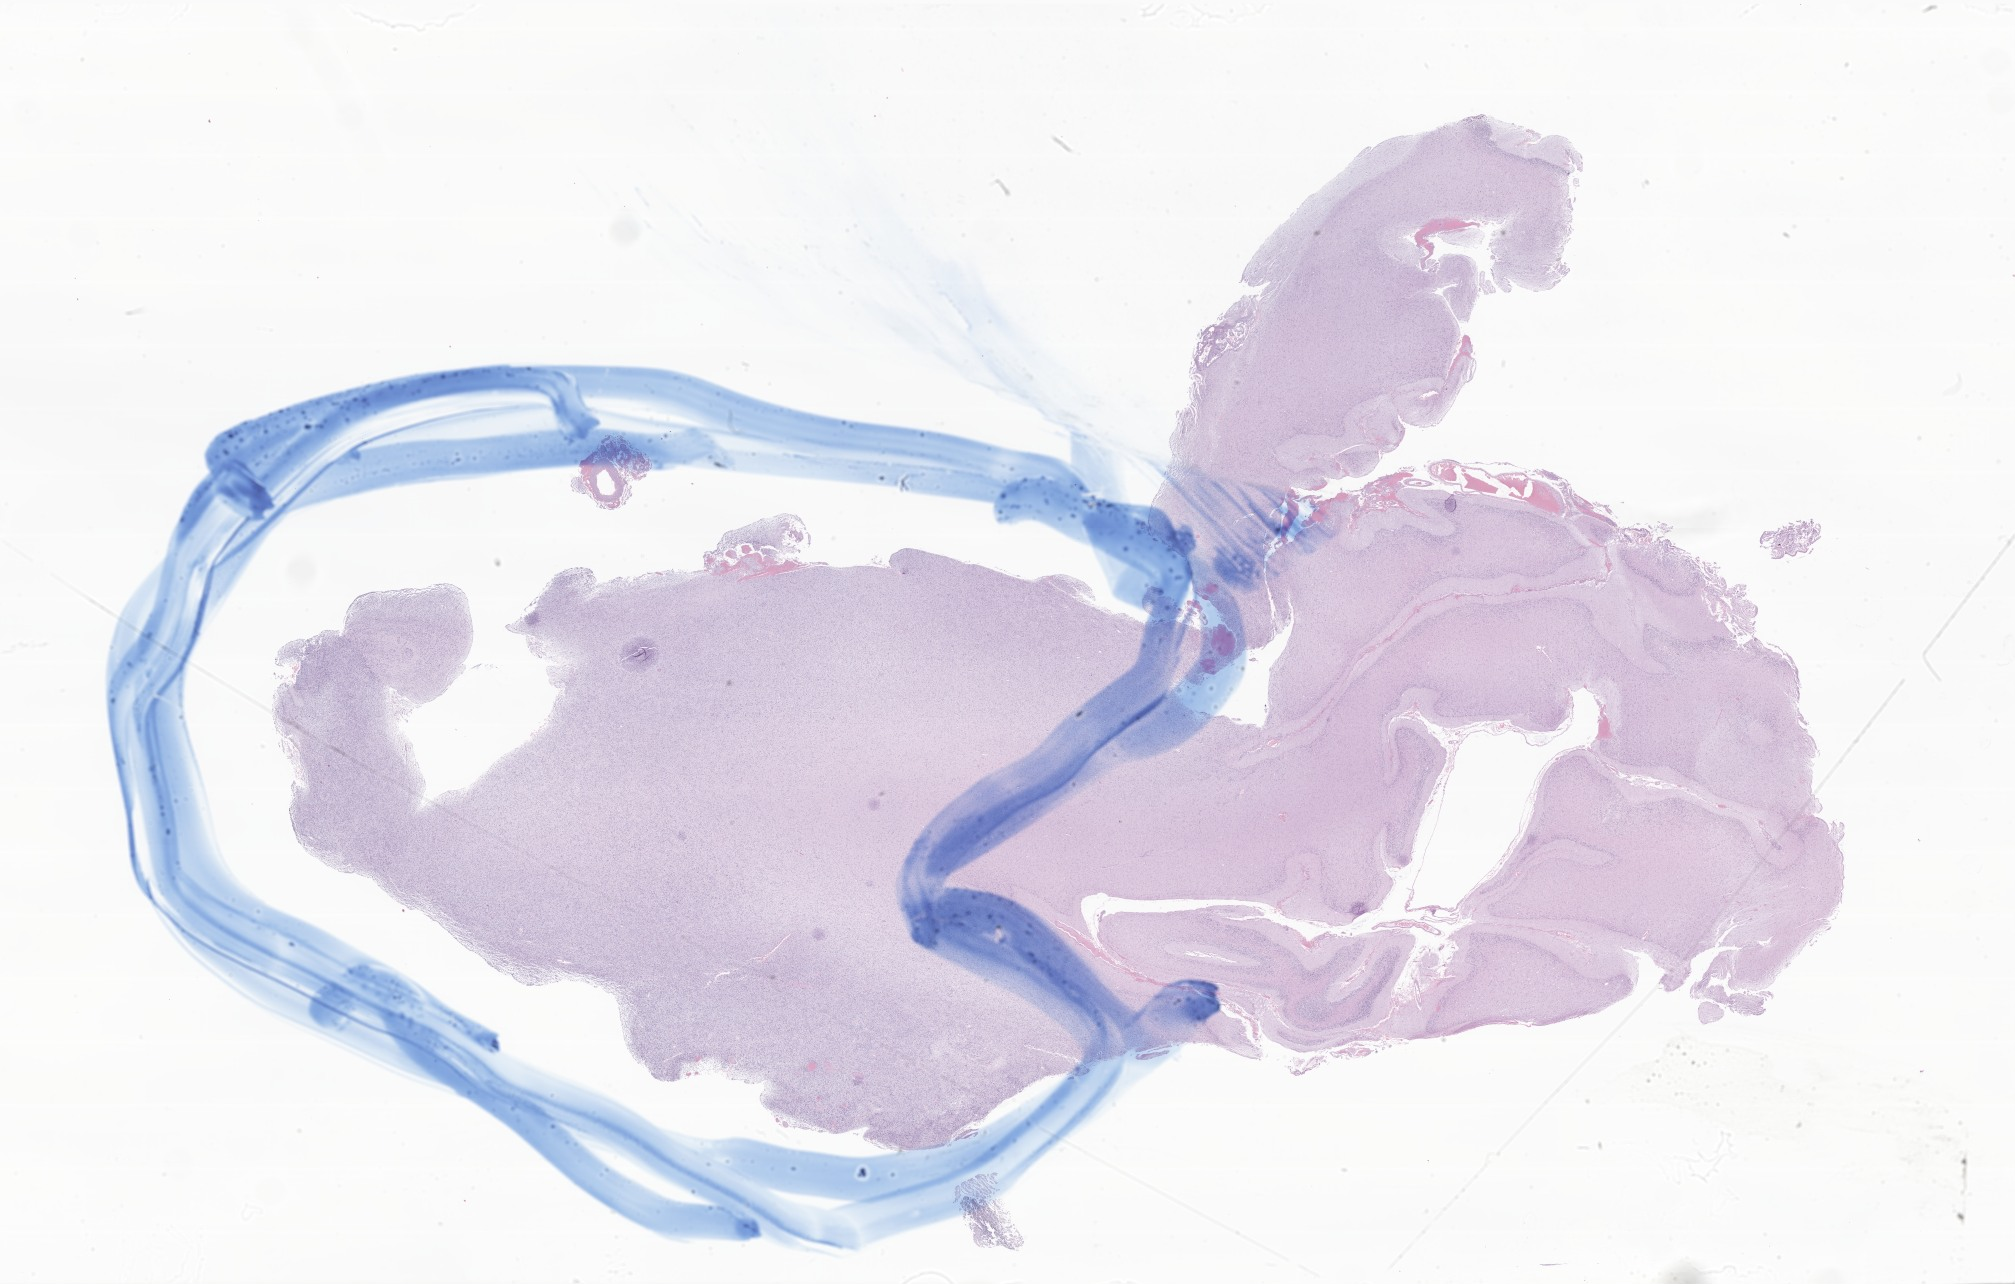
Whole-slide image, hematoxylin and eosin (H&E) stain of tumor tissue from the brain — a low-resolution overview of the entire scanned area, about 34.0 x 21.7 mm, formalin-fixed paraffin-embedded section. Patient: male, age 91 months.
- recorded diagnosis: Glioma, malignant